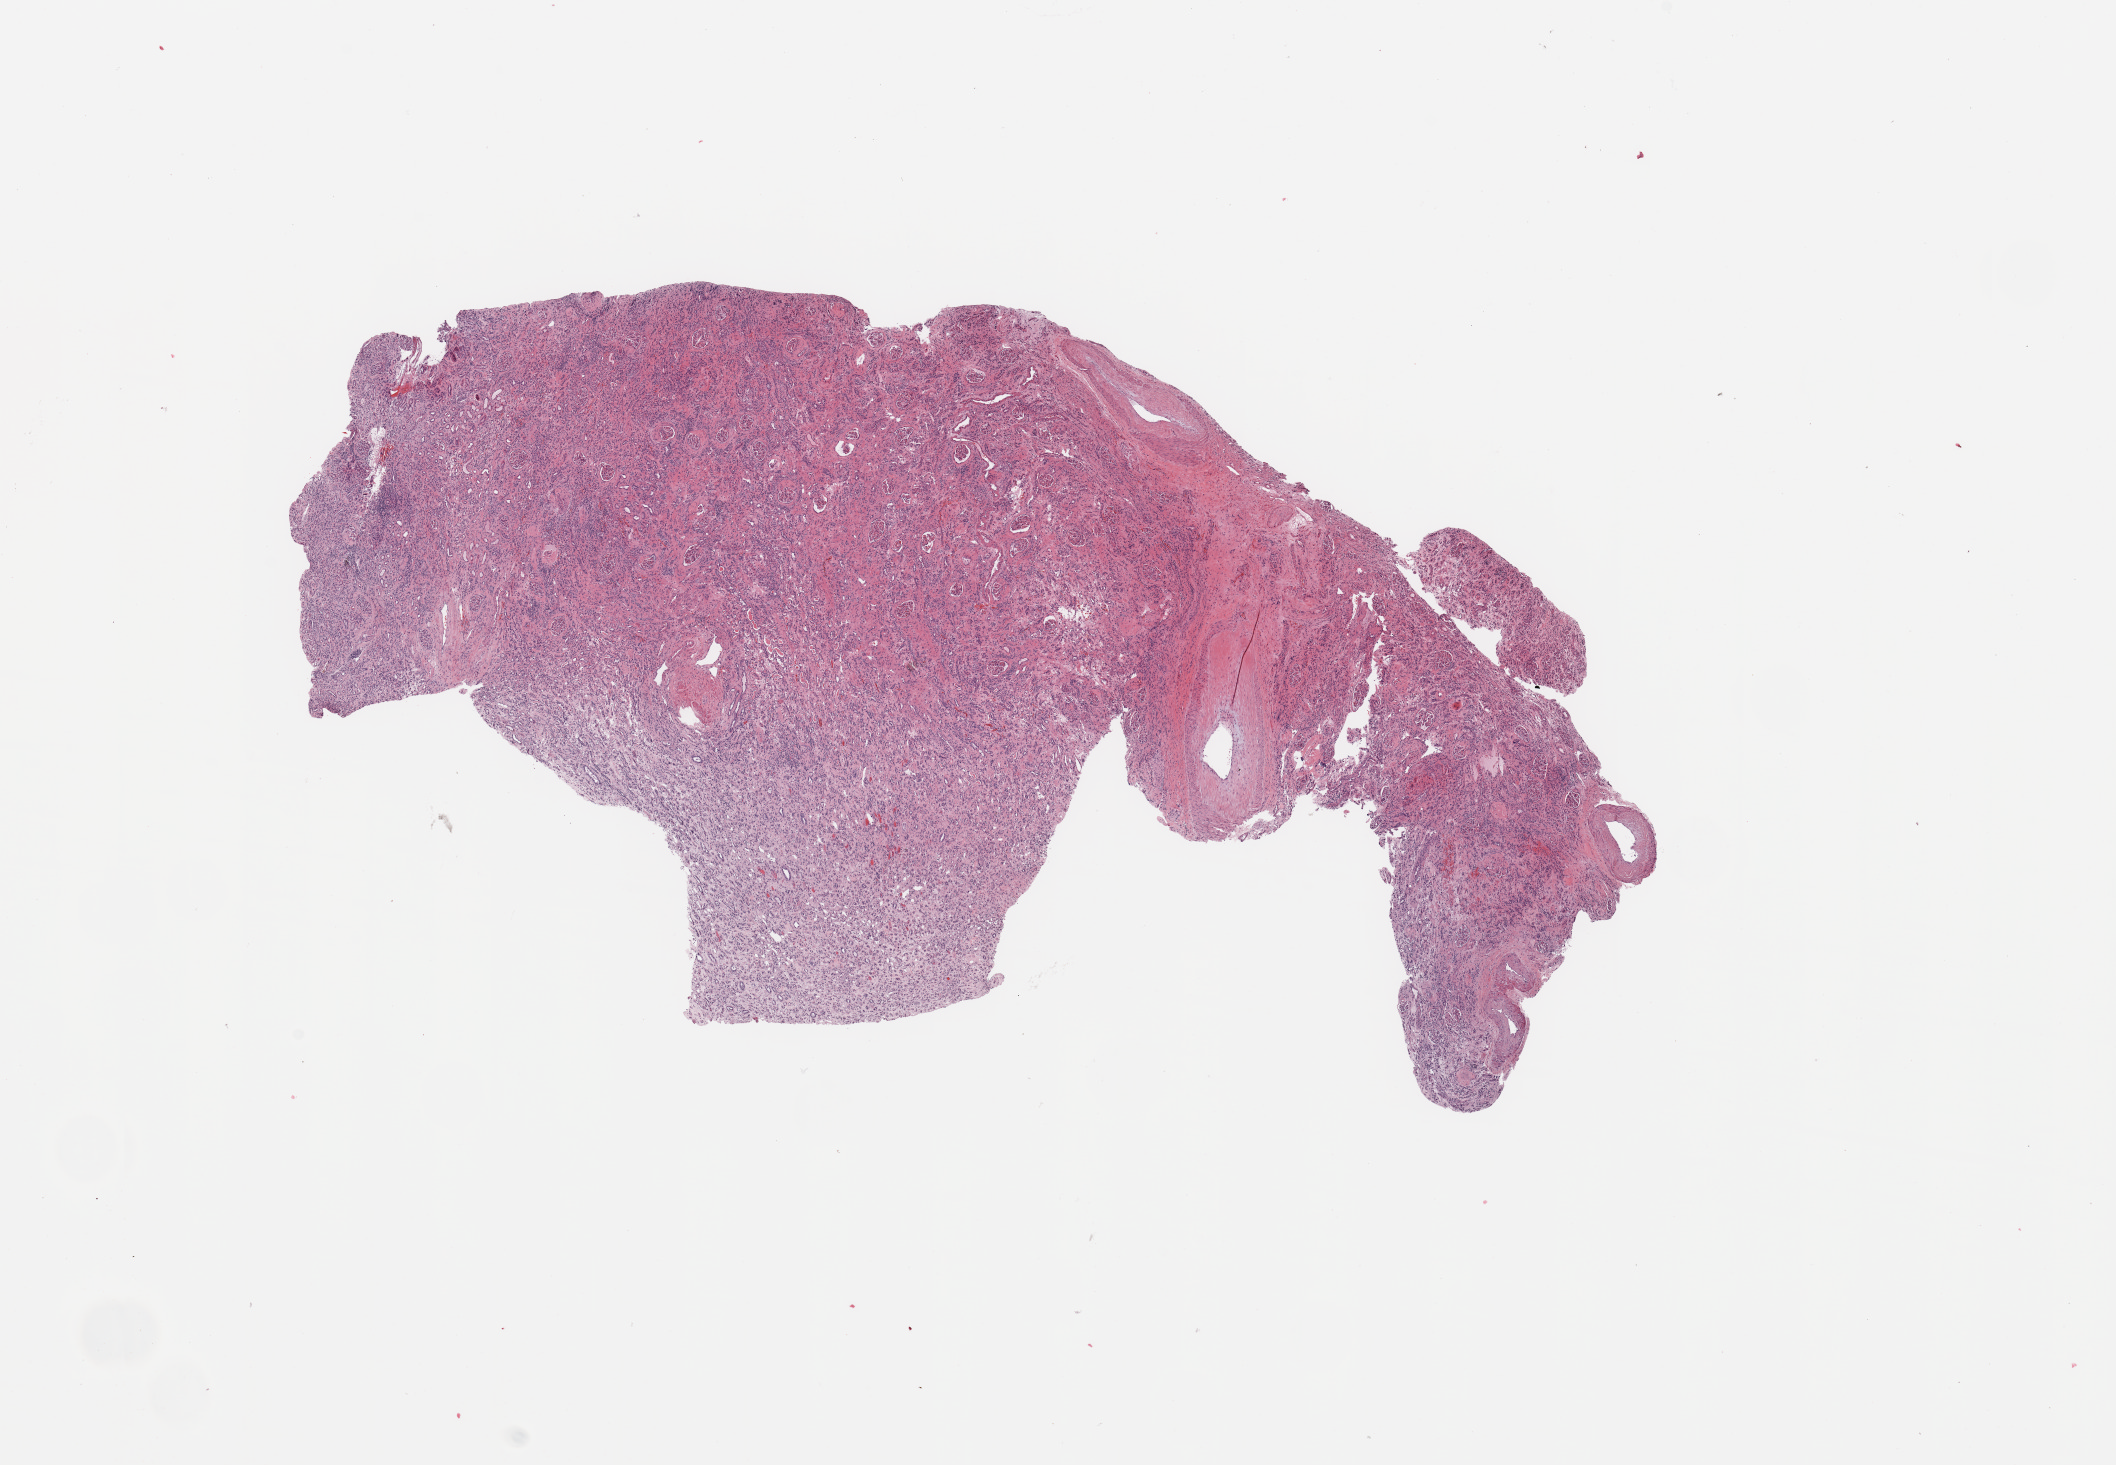
Whole-slide histology image, H&E, shown as a low-resolution overview of the whole scanned area (about 16.7 x 11.6 mm, from a 20x scan), normal (non-tumour) tissue sample, sampled site: kidney. Patient: female, age 56 years.
• this section: normal (non-tumour) tissue from the same patient
• patient diagnosis: Renal cell carcinoma, NOS